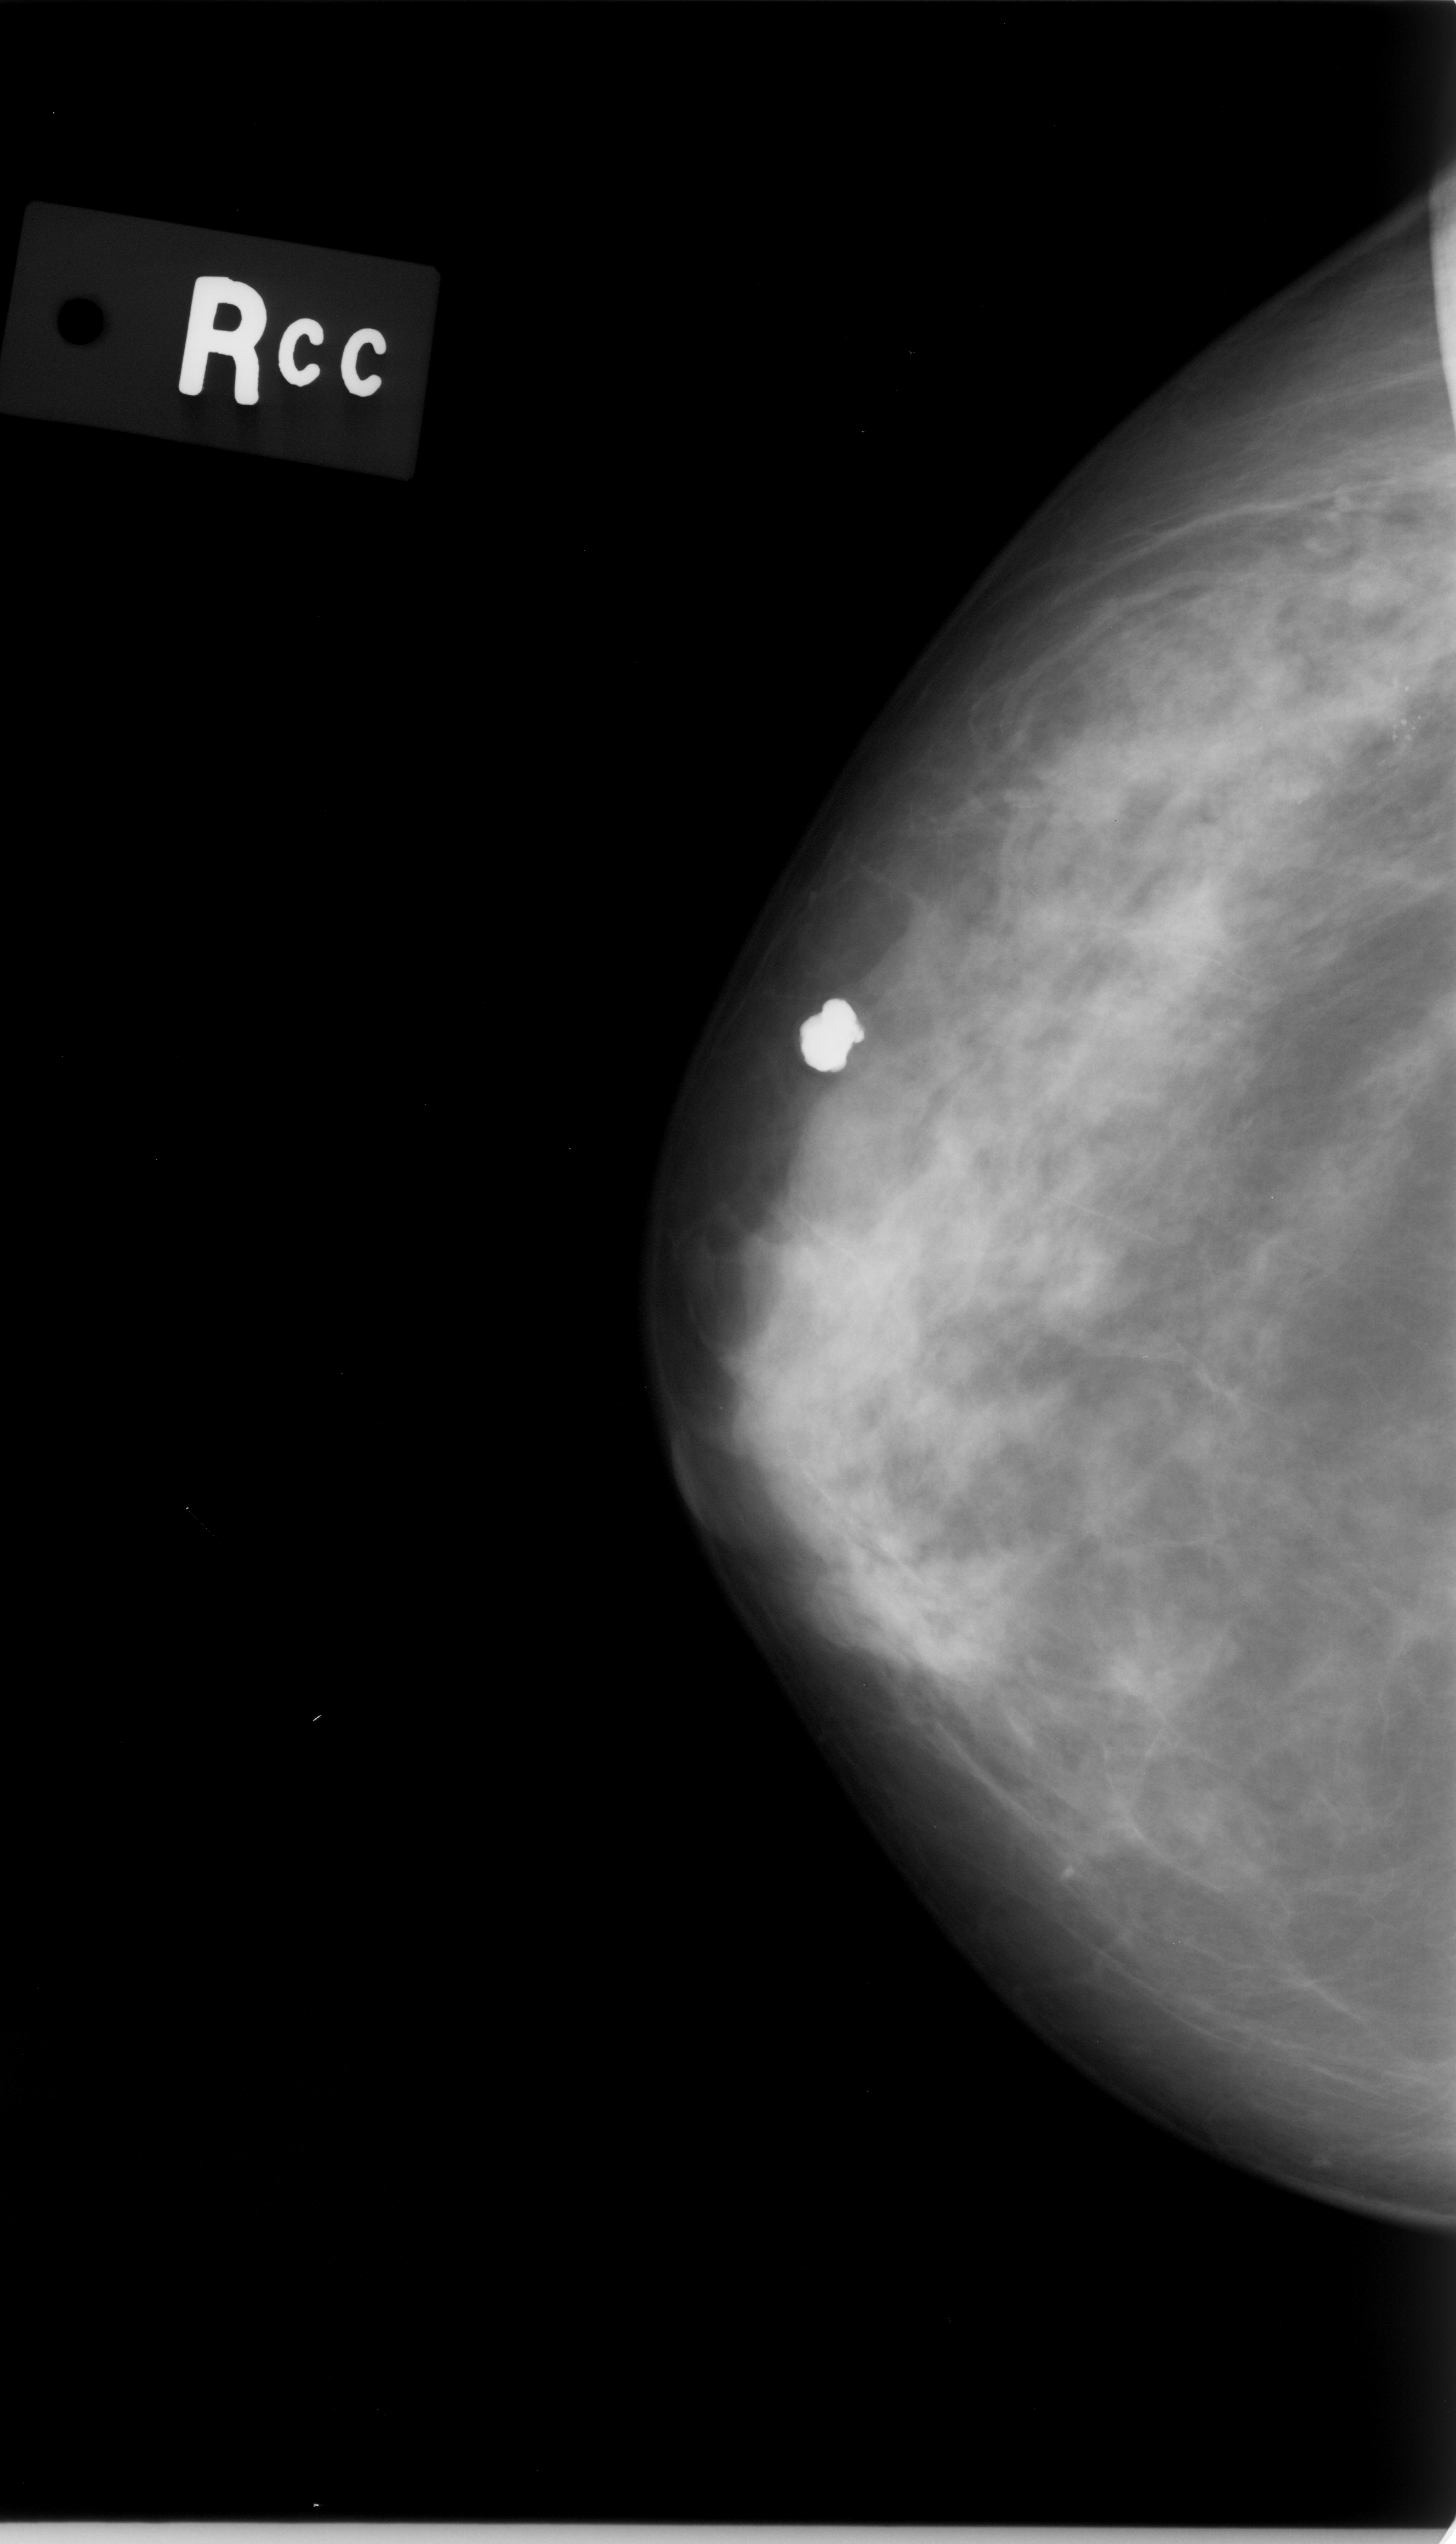
Scanned film-screen mammogram, right breast, craniocaudal (CC) view.
Calcifications, morphology pleomorphic, distribution clustered; BI-RADS assessment category 5; subtlety rating 4 on a 1 (subtle) to 5 (obvious) scale; pathology (as recorded): malignant.